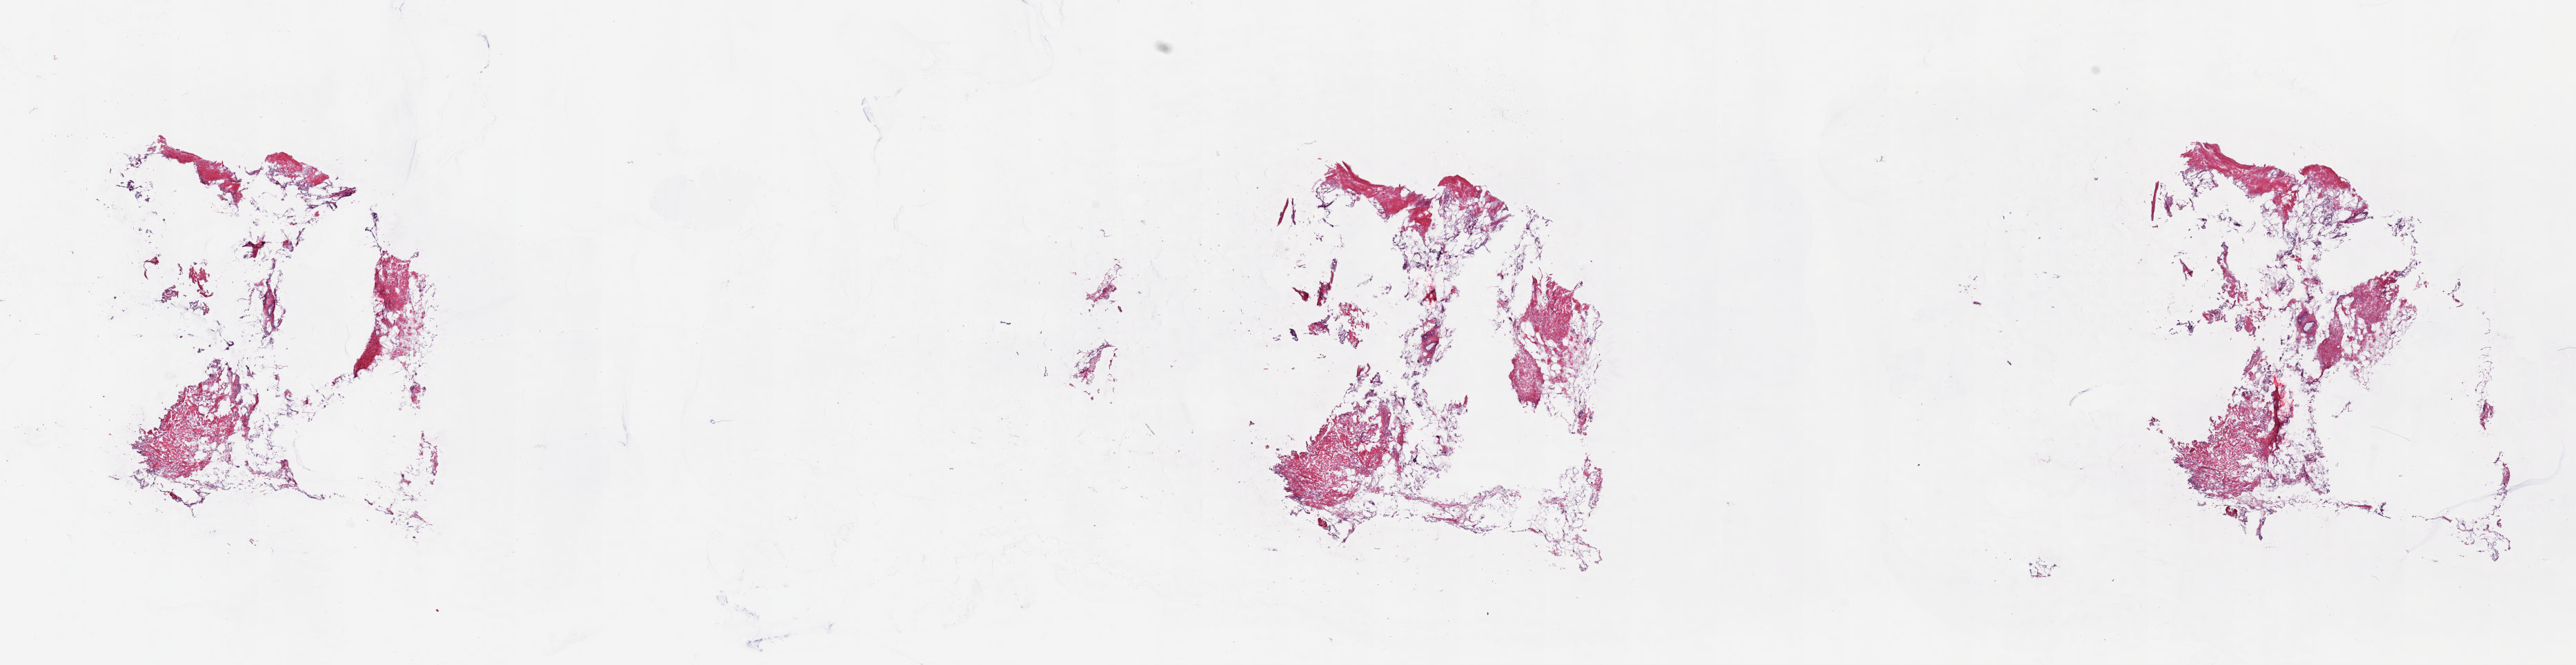
Whole-slide histology image, H&E-stained, a low-resolution overview of the entire scanned area, about 29.4 x 7.6 mm (from a 20x scan); frozen section from the top of the tissue portion; connective, subcutaneous and other soft tissues, solid tissue normal (non-tumour tissue) sample. Male patient; age at initial diagnosis 42 years. Slide review estimates, as recorded: tumour cells 0%, tumour nuclei 0%, normal cells 100%, stromal cells 0%, necrosis 0%. Inflammatory infiltration, as recorded: lymphocyte infiltration 1%, monocyte infiltration 0%, neutrophil infiltration 0%.
This section: solid tissue normal (non-tumour) sample from the same patient. Patient diagnosis: Leiomyosarcoma, NOS (connective, subcutaneous and other soft tissues of lower limb and hip).